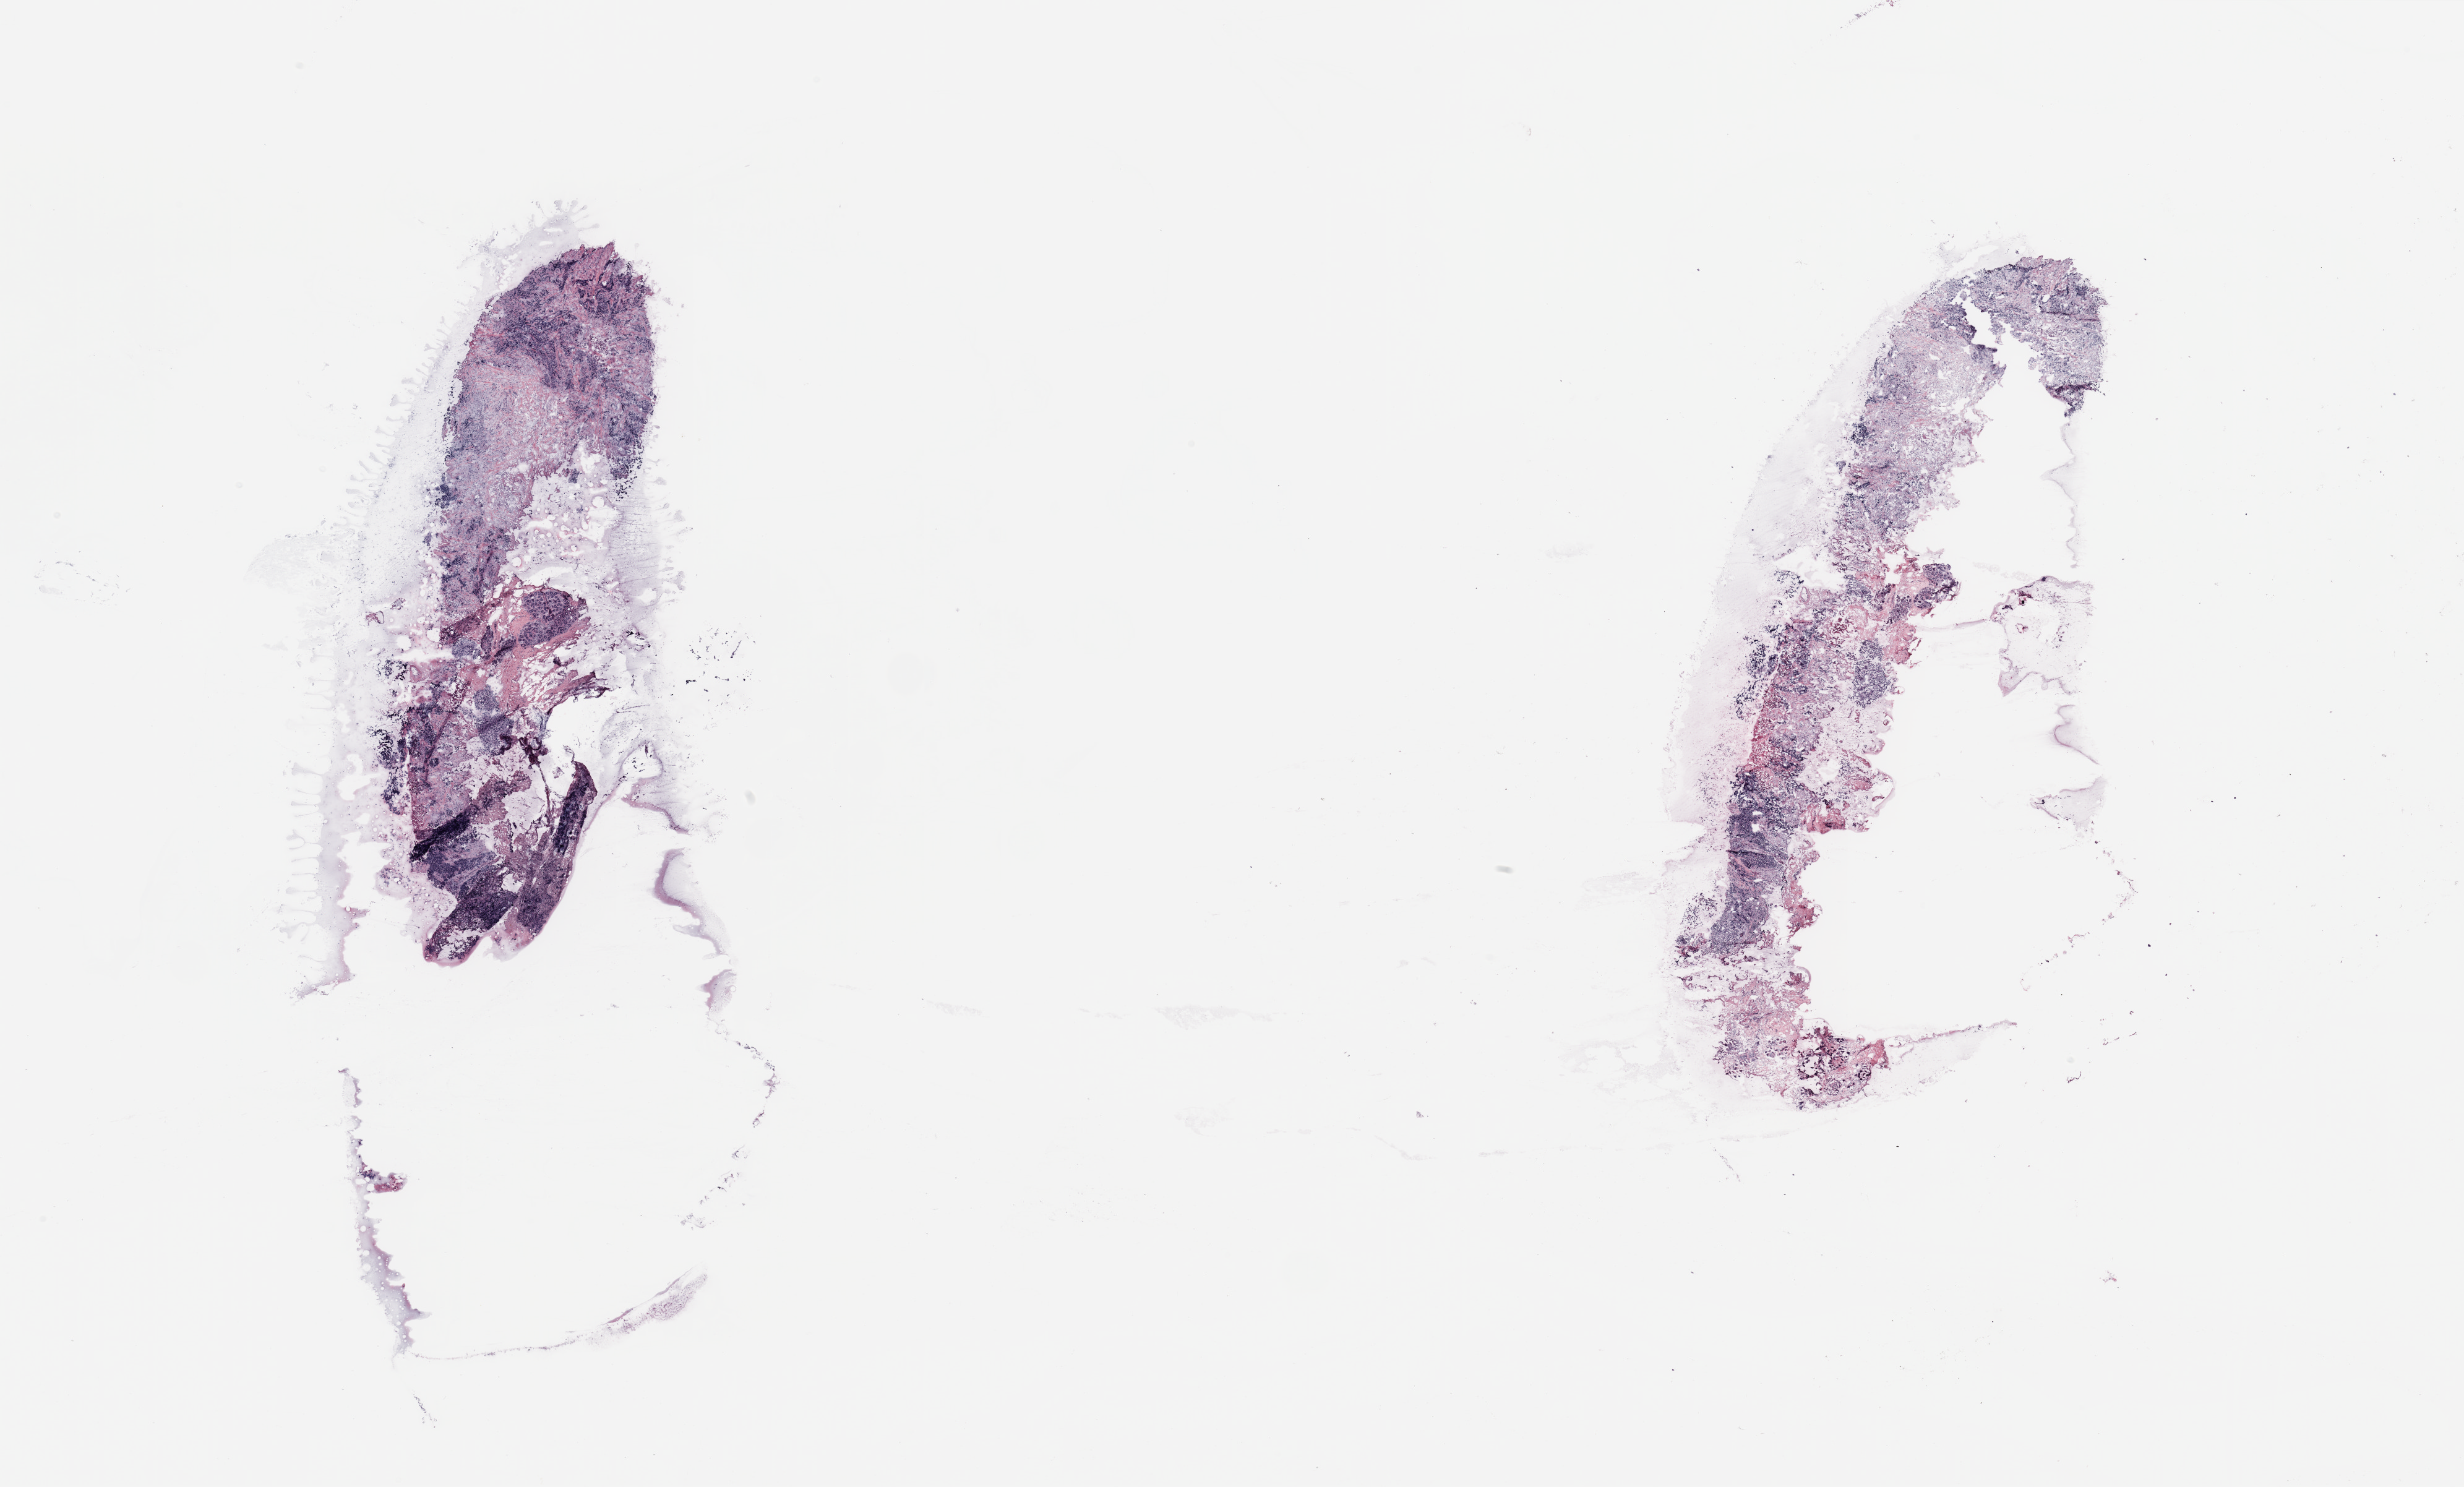
Digitized H&E-stained tissue section (whole slide), whole scanned area (about 31.5 x 19.0 mm) shown as a low-resolution overview. Patient: female, age 45 years.
Specimen: tumour tissue sample, breast.